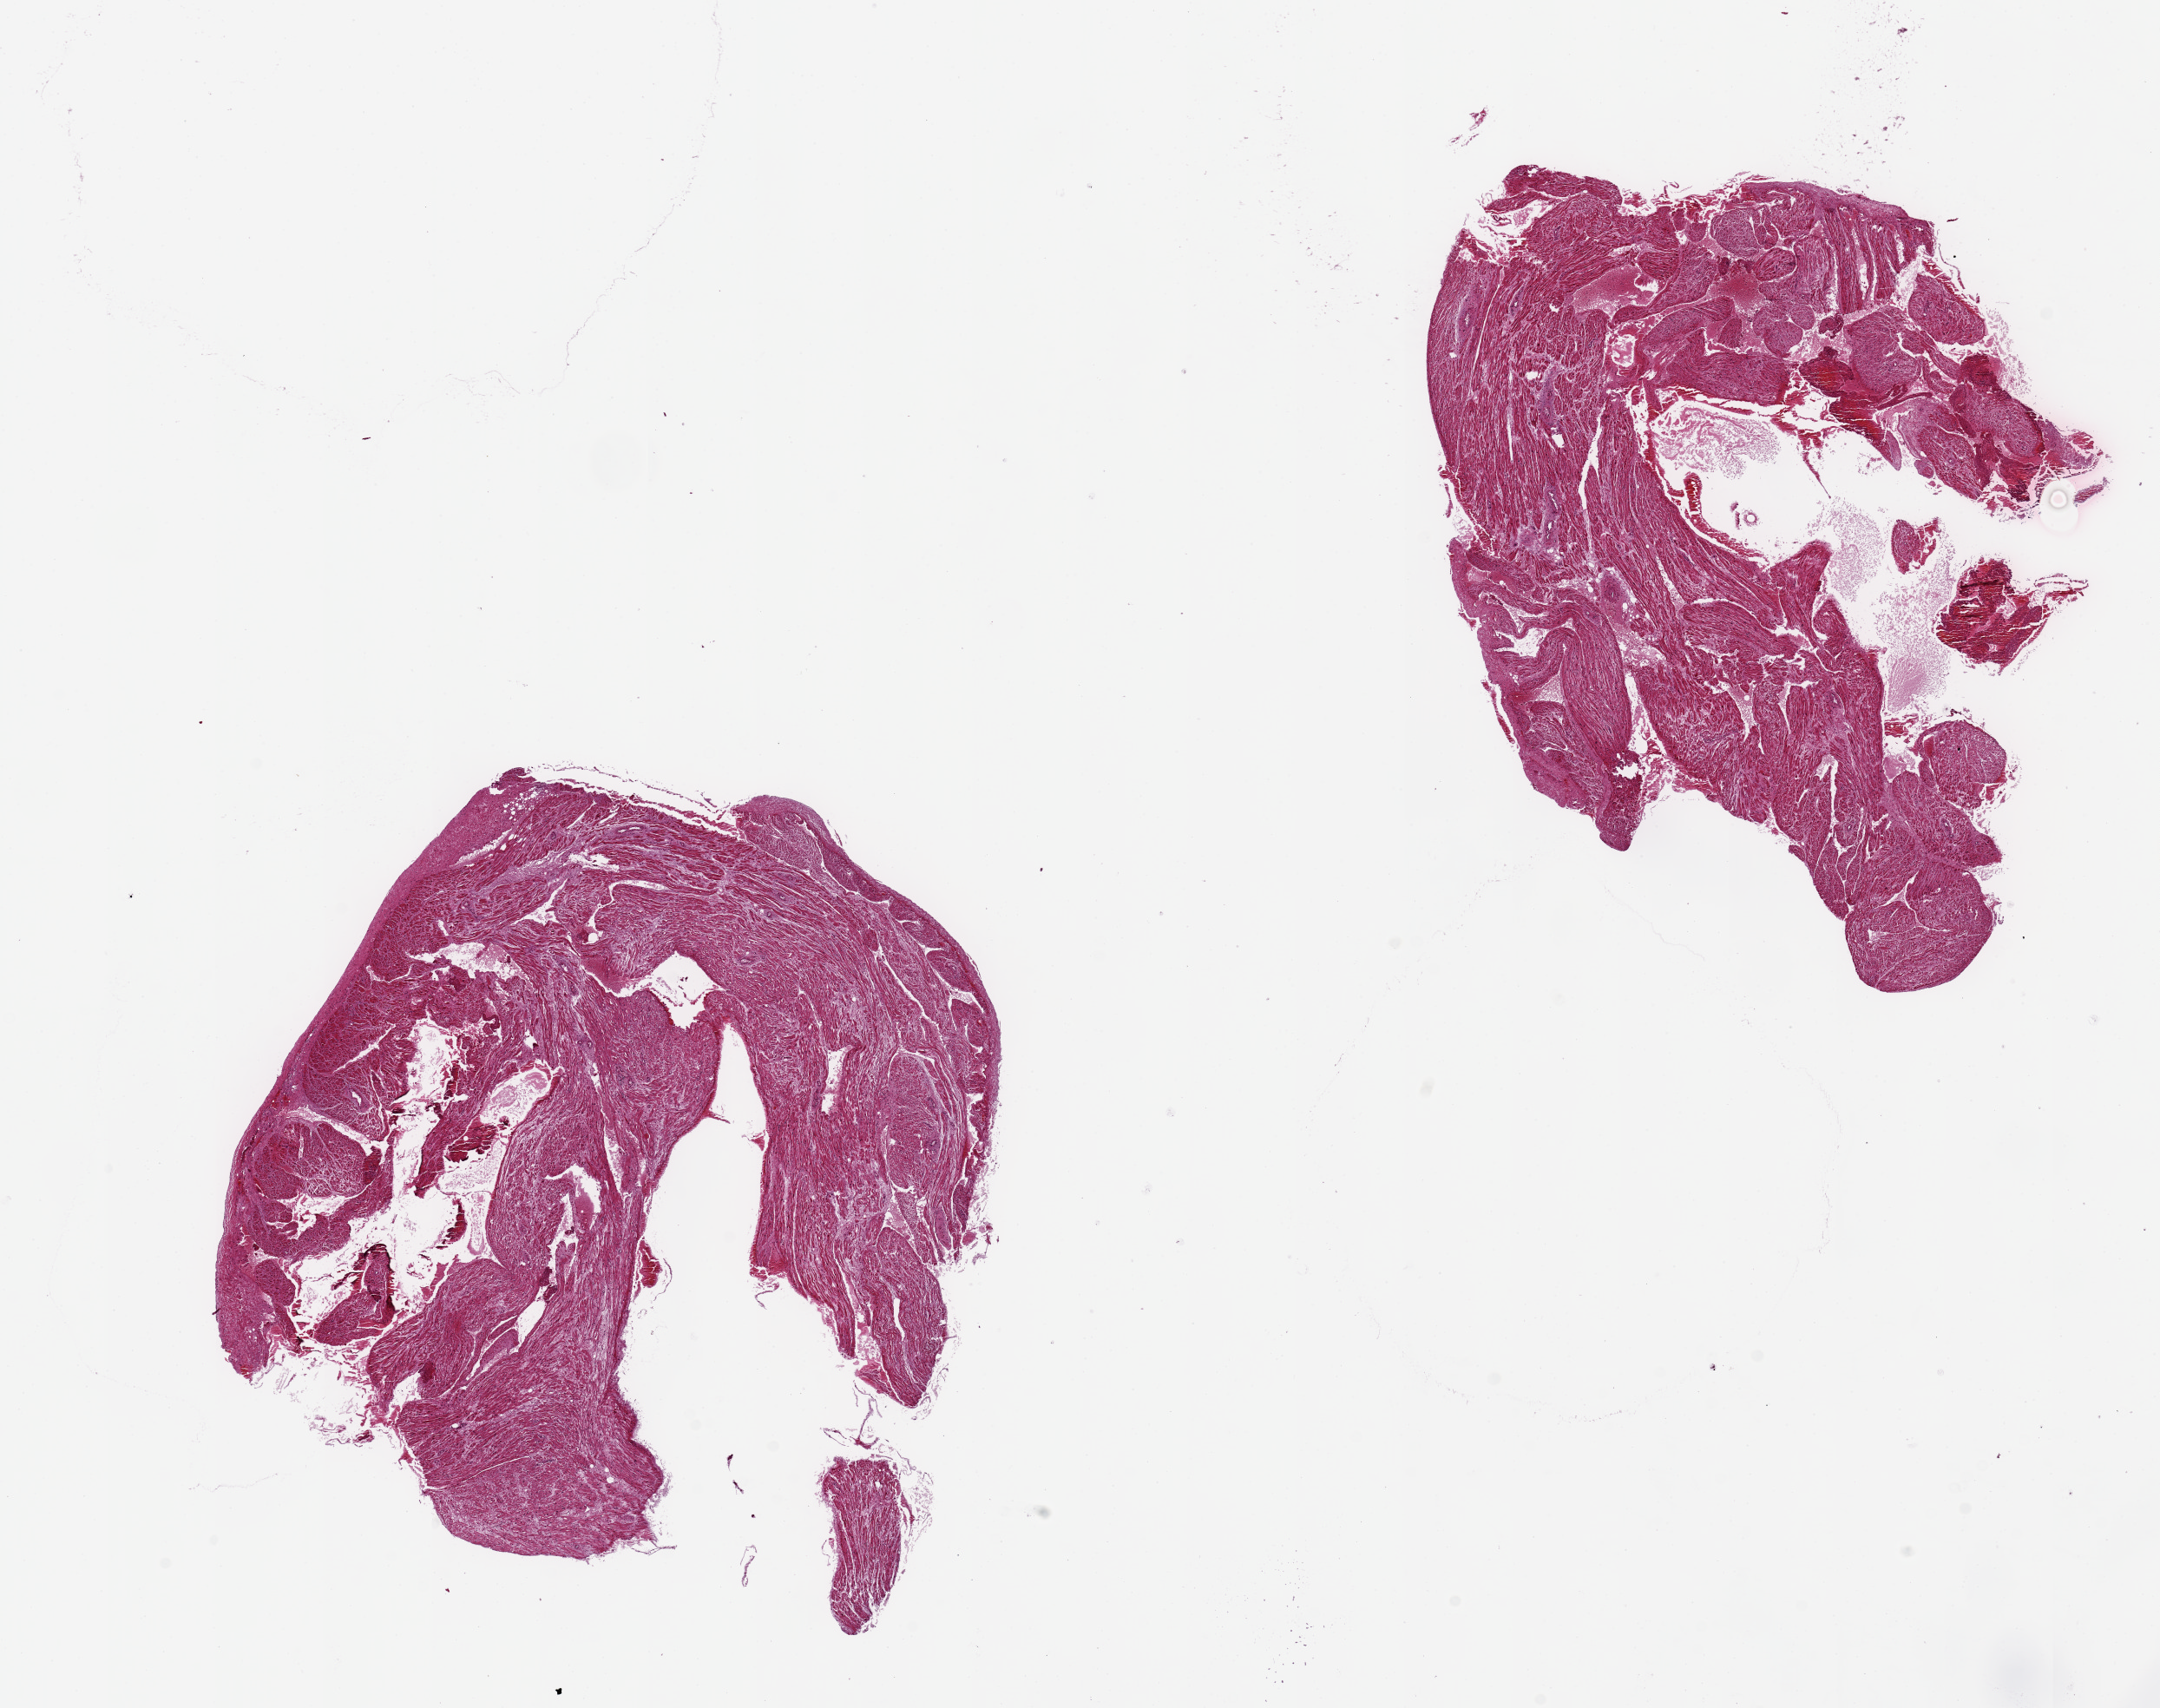
Haematoxylin and eosin whole-slide image — shown as a low-resolution overview of the whole scanned area (about 19.7 x 15.6 mm), PAXgene-fixed, paraffin-embedded tissue, target tissue: auricular appendage, donor tissue sample. Donor sex: female.
- reviewer comment on this tissue sample: 2 pieces. 8x7& 9x6mm